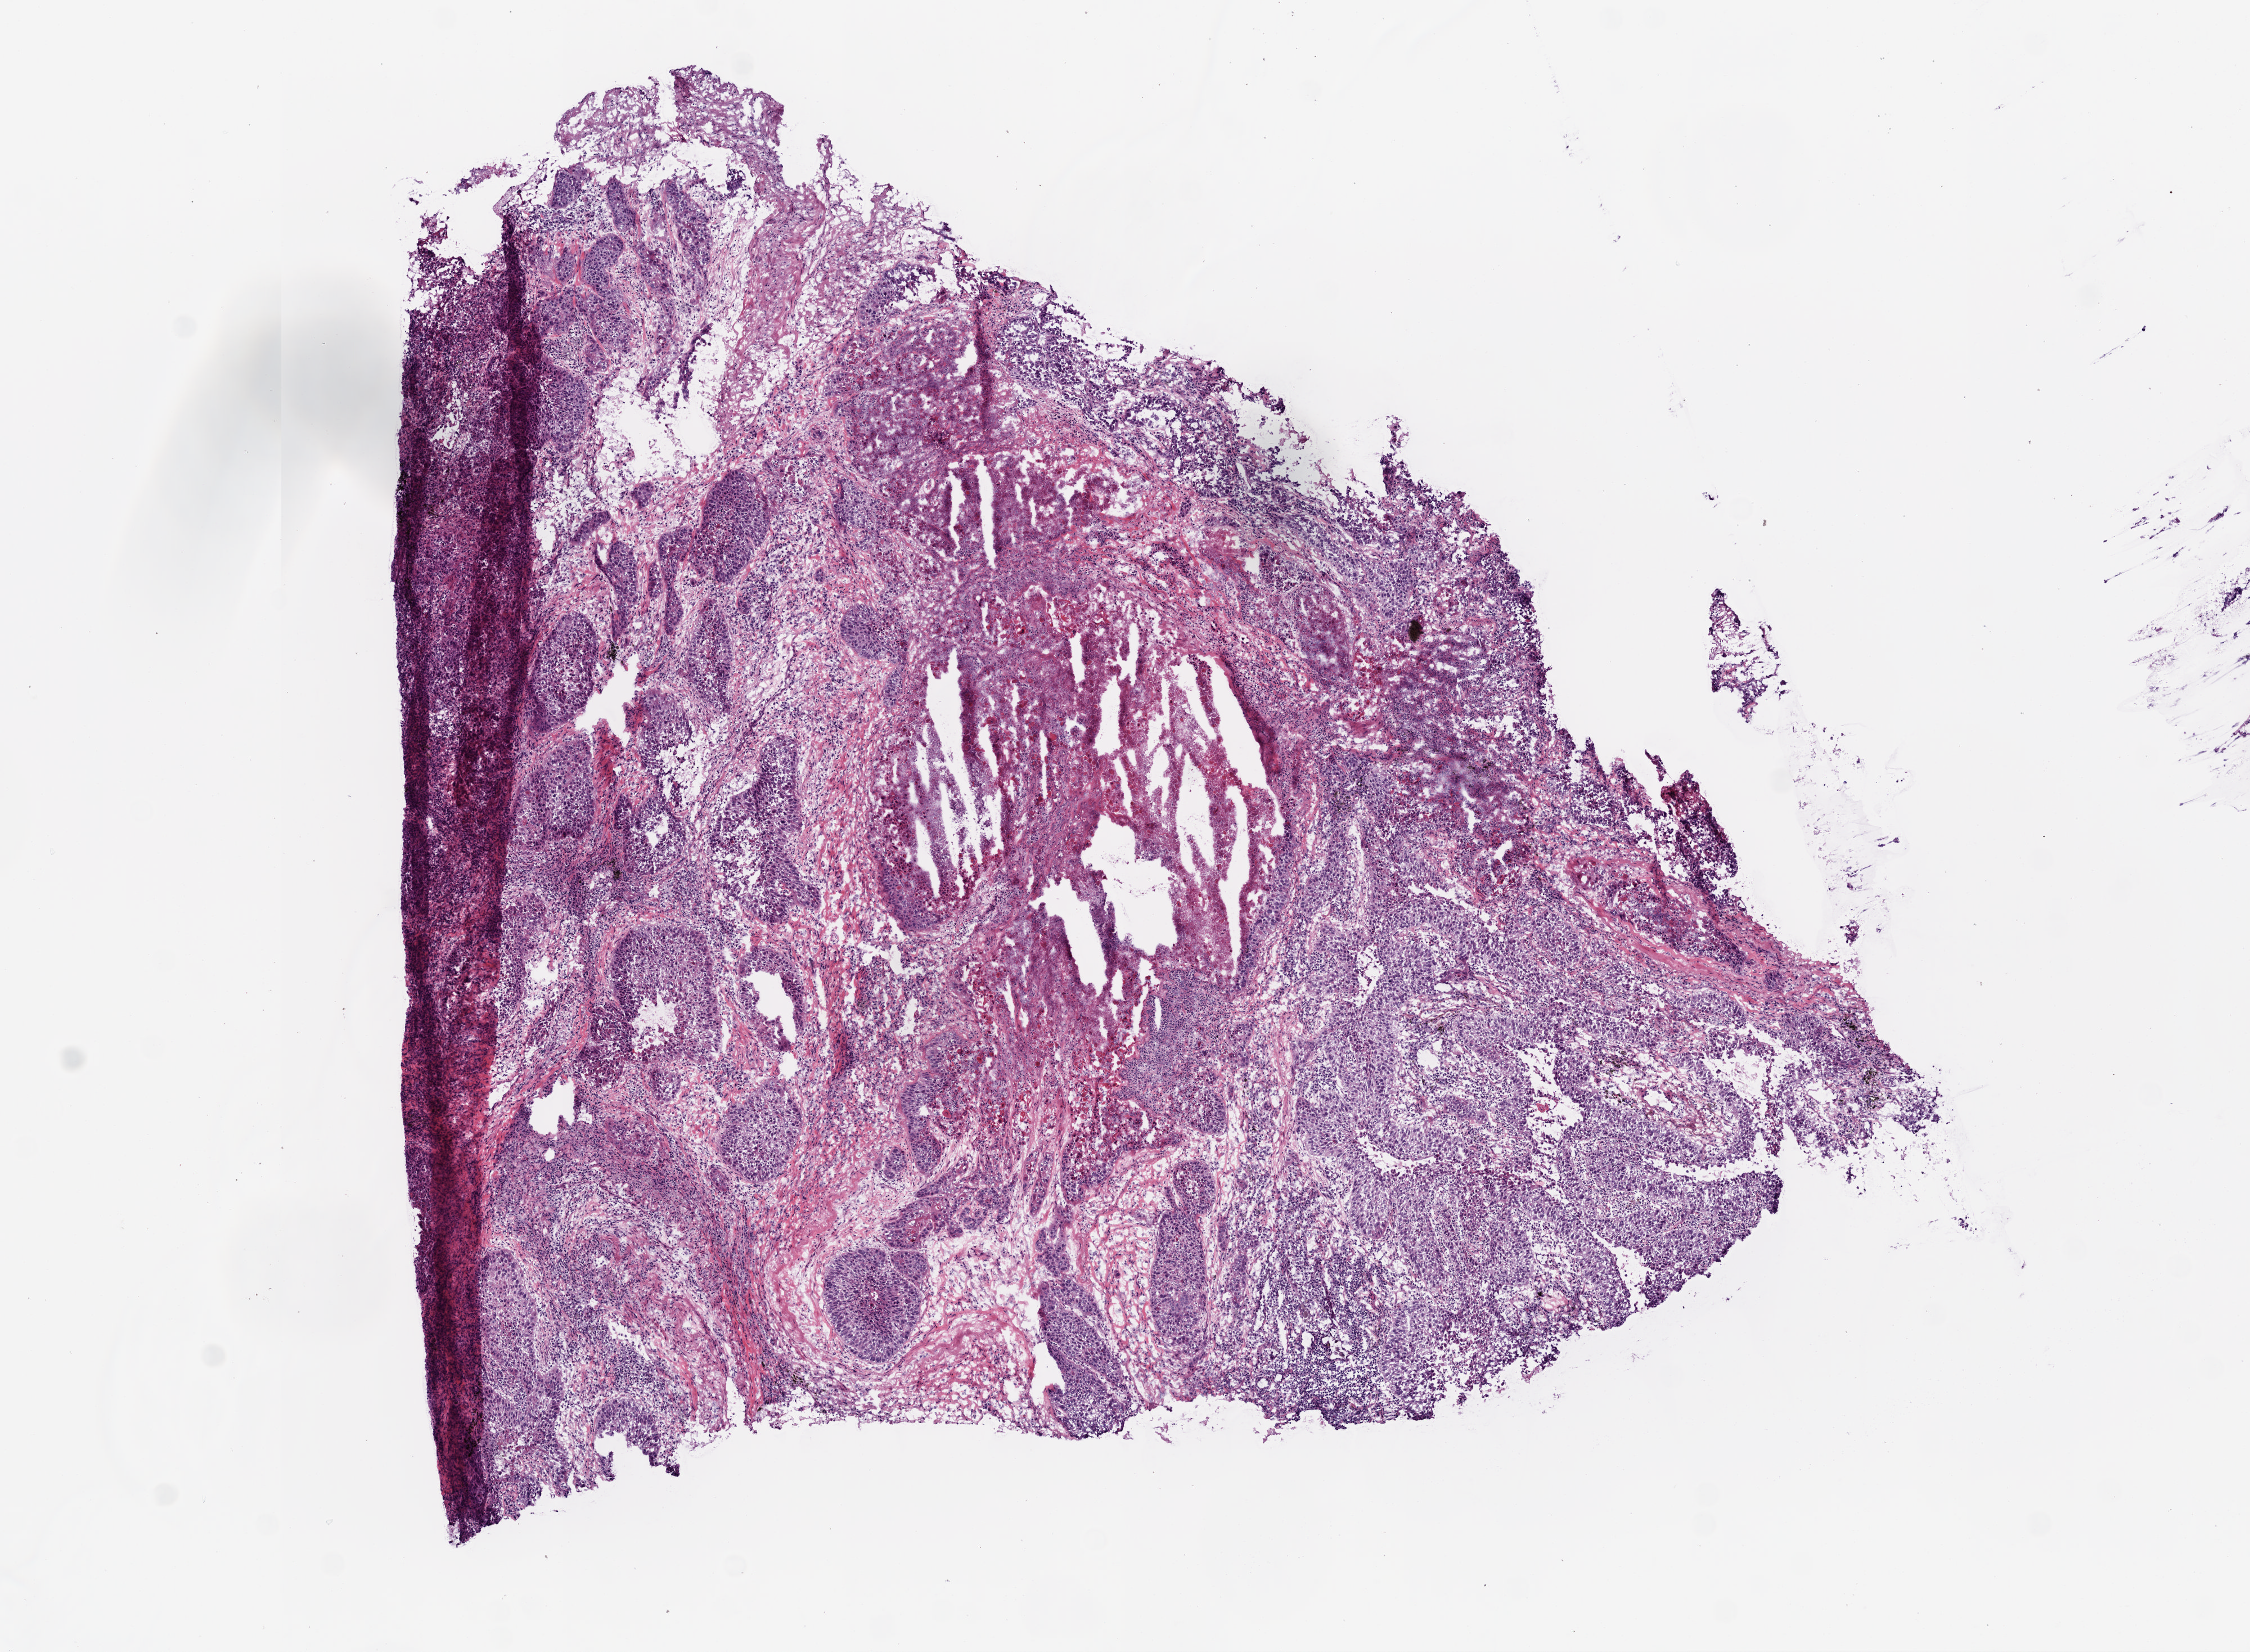
Digitized H&E-stained tissue section (whole slide) — whole scanned area (about 8.0 x 5.9 mm, from a 20x scan) shown as a low-resolution overview. Frozen section from the top of the tissue portion. Lung, primary tumour sample. Male patient; age at initial diagnosis 66 years. Composition of this section per pathologist review: tumour cells 65%, tumour nuclei 70%, normal cells 0%, stromal cells 15%, necrosis 20%.
• laterality: left
• AJCC pathologic stage: IB (6th edition)
• histologic diagnosis: Squamous cell carcinoma, NOS (upper lobe, lung)